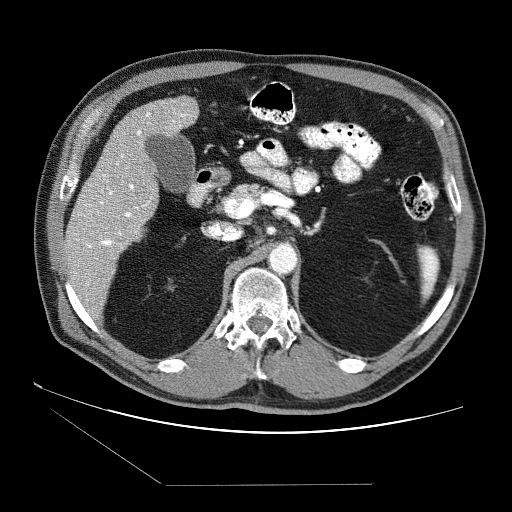
Contrast-enhanced abdominal CT (liver protocol), one axial slice; position 35 of 87 along the scan axis; reconstruction kernel STANDARD; soft-tissue window (W 400 / L 40 HU); 2.5 mm slice thickness; 512 × 512 image matrix, field of view 400 × 400 mm. Case-level facts recorded for this patient, not image findings: diagnosis: hepatocellular carcinoma (patient treated with transarterial chemoembolisation; whether this scan precedes or follows treatment is not stated here); TNM stage (as recorded): Stage-II; Child-Pugh class: B; tumour differentiation: no biopsy; tumour nodularity: multinodular.
Annotated regions visible in this slice (semi-automatic segmentation, software-assisted and operator-edited):
- liver parenchyma outside the tumour (the mass and vessels are separate outlines, so this box may not span the whole liver): bounding box <64,96,198,310> (left, top, right, bottom; pixels)
- liver vessels: <77,112,187,285>